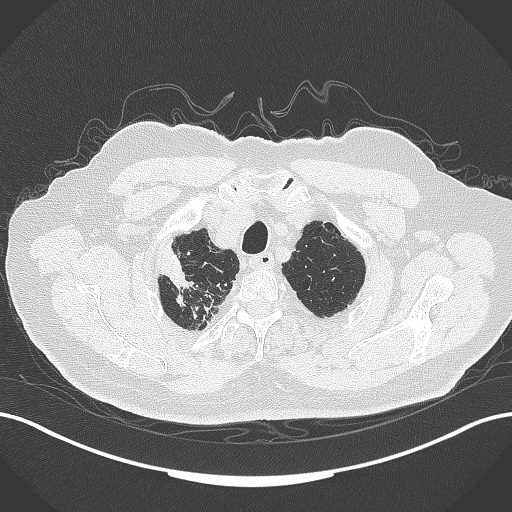
Chest CT, one axial slice. Lung window (W 1500 / L -600 HU). 1 mm slice thickness. 512 × 512 image matrix, field of view 400 × 400 mm. Patient: male, 72 years. Case-level facts recorded for this patient, not image findings: clinical TNM (as recorded): T1a N0 M0.
Structures marked on this image (bounding box drawn by a radiologist):
- lung tumour (recorded histology: squamous cell carcinoma): bounding box <158,237,197,293> (left, top, right, bottom; pixels)